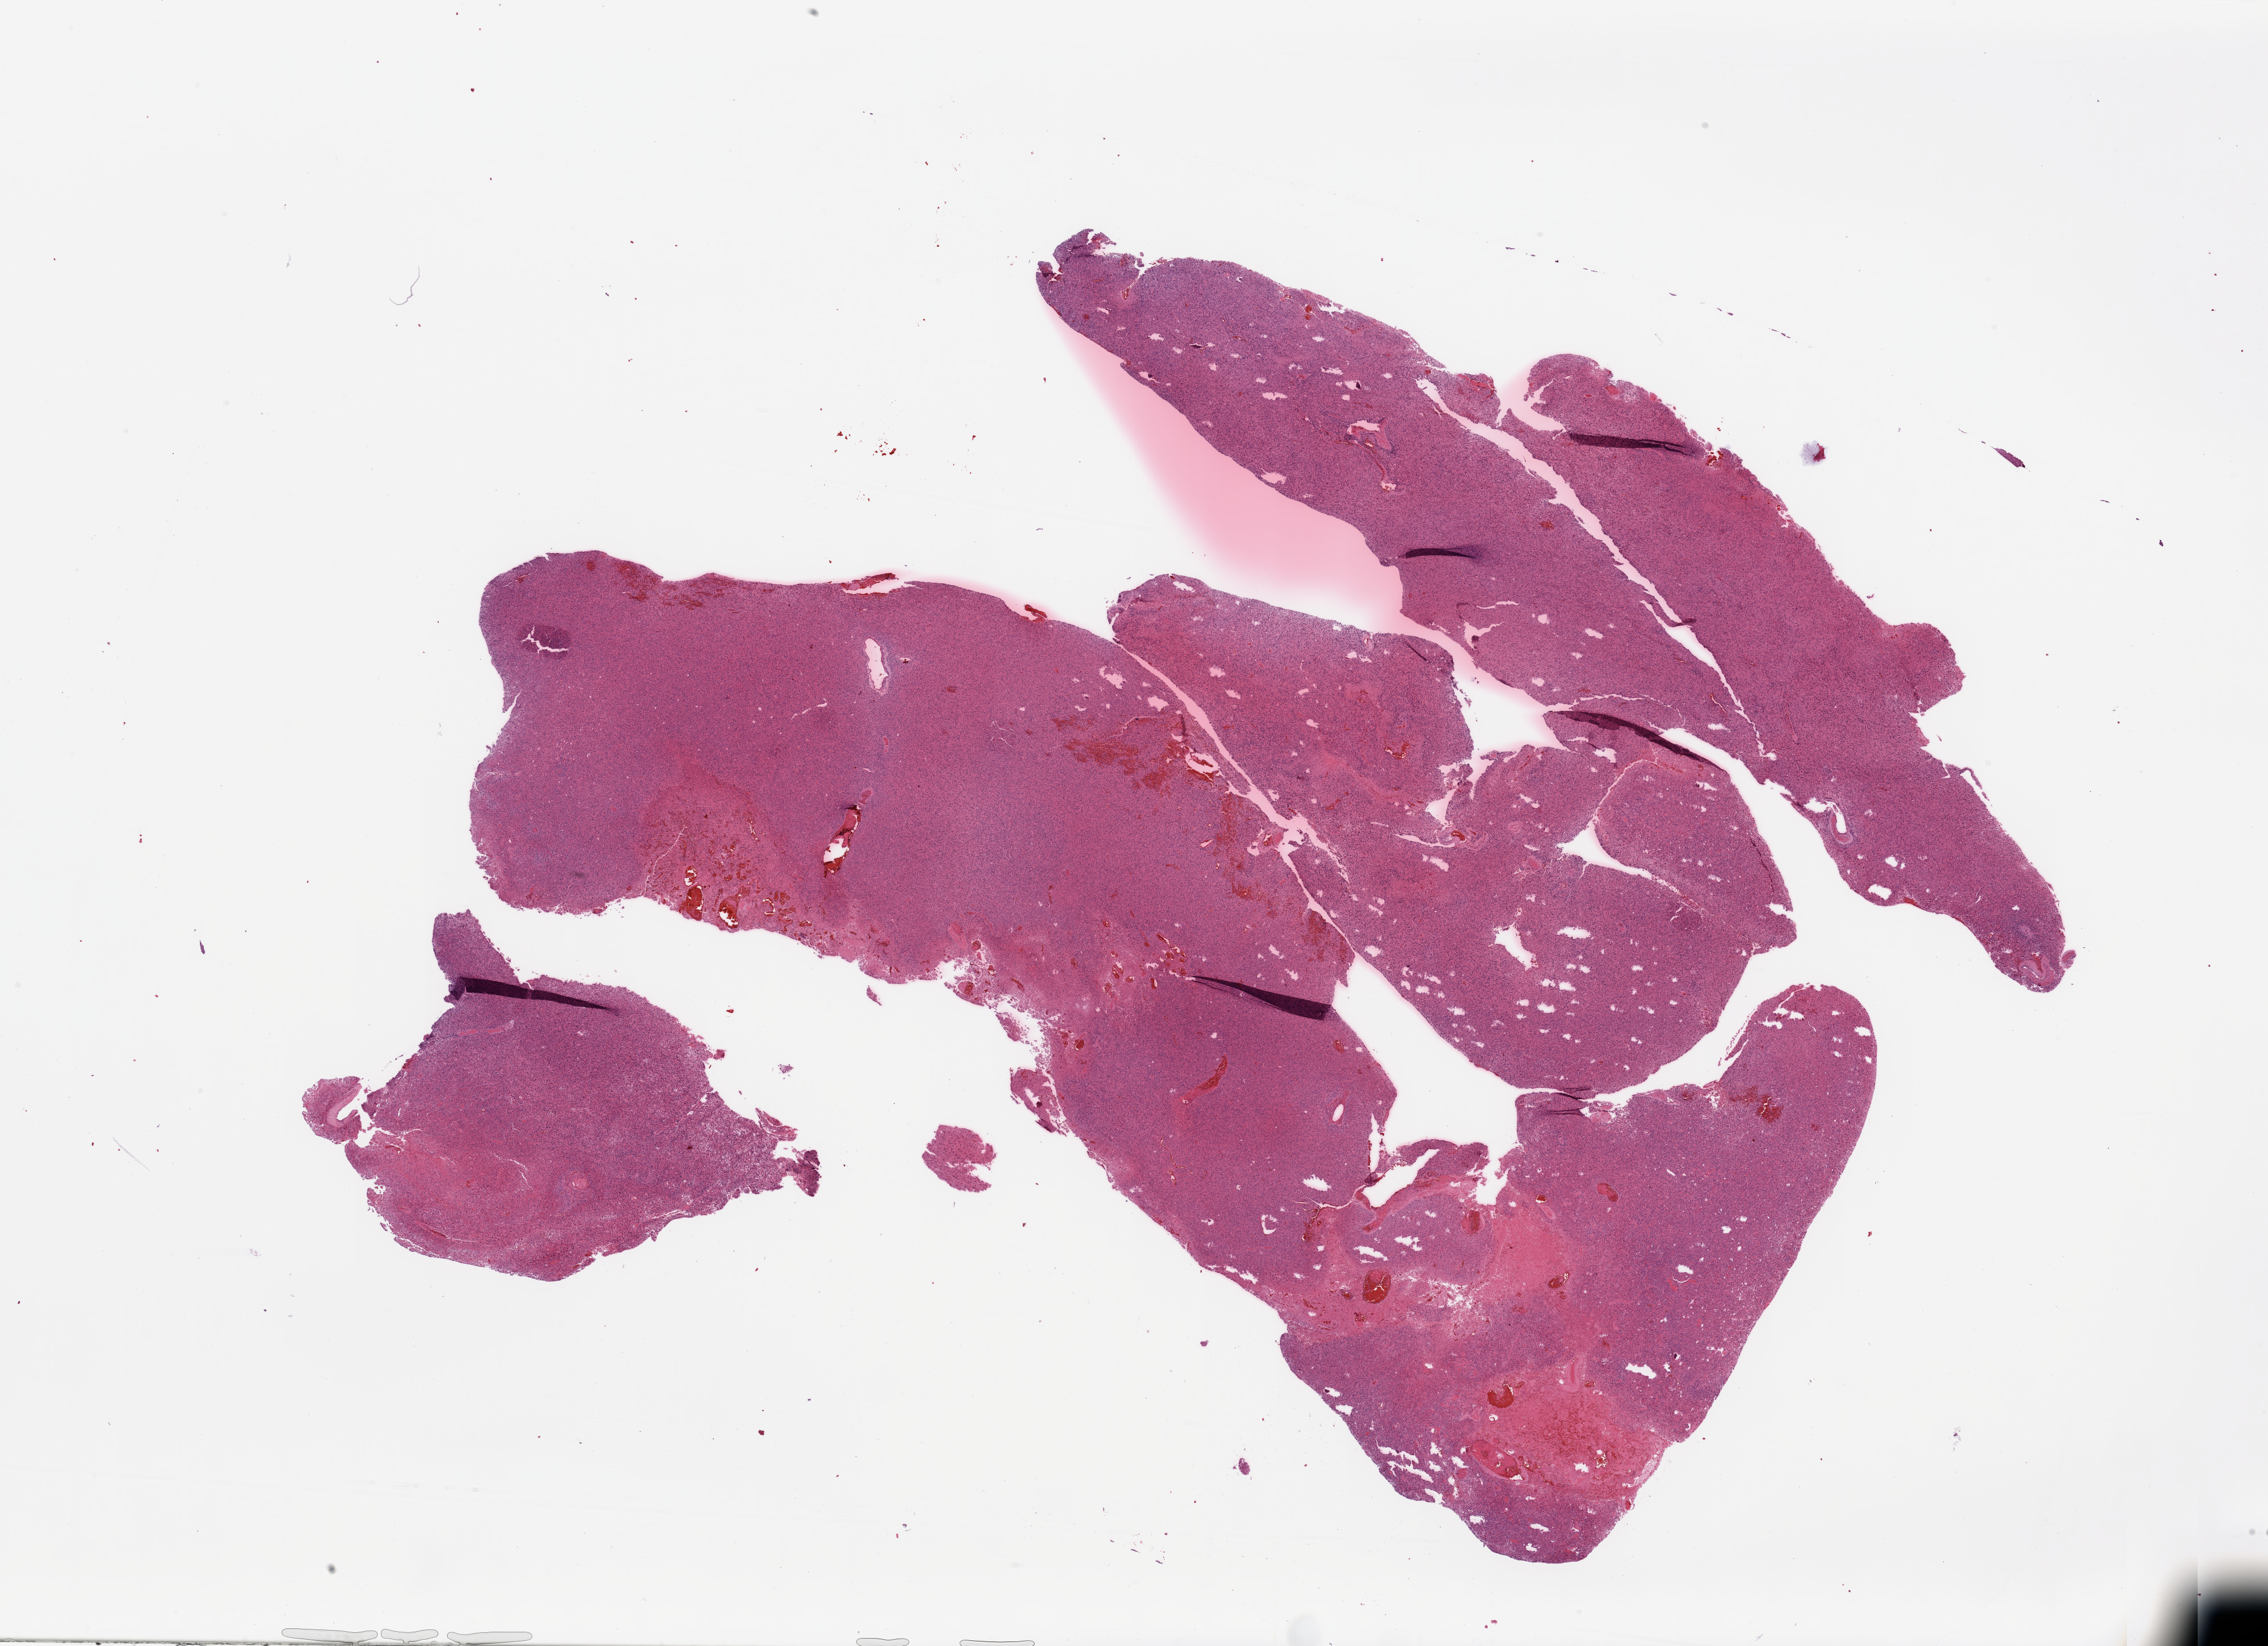
Hematoxylin and eosin (H&E) stained whole-slide image, a low-resolution overview of the entire scanned area, about 31.5 x 22.9 mm, tumour tissue sample, brain. Patient: female, age 63 years.
* primary tumour site (as recorded): parietal lobe
* histologic diagnosis: Glioblastoma